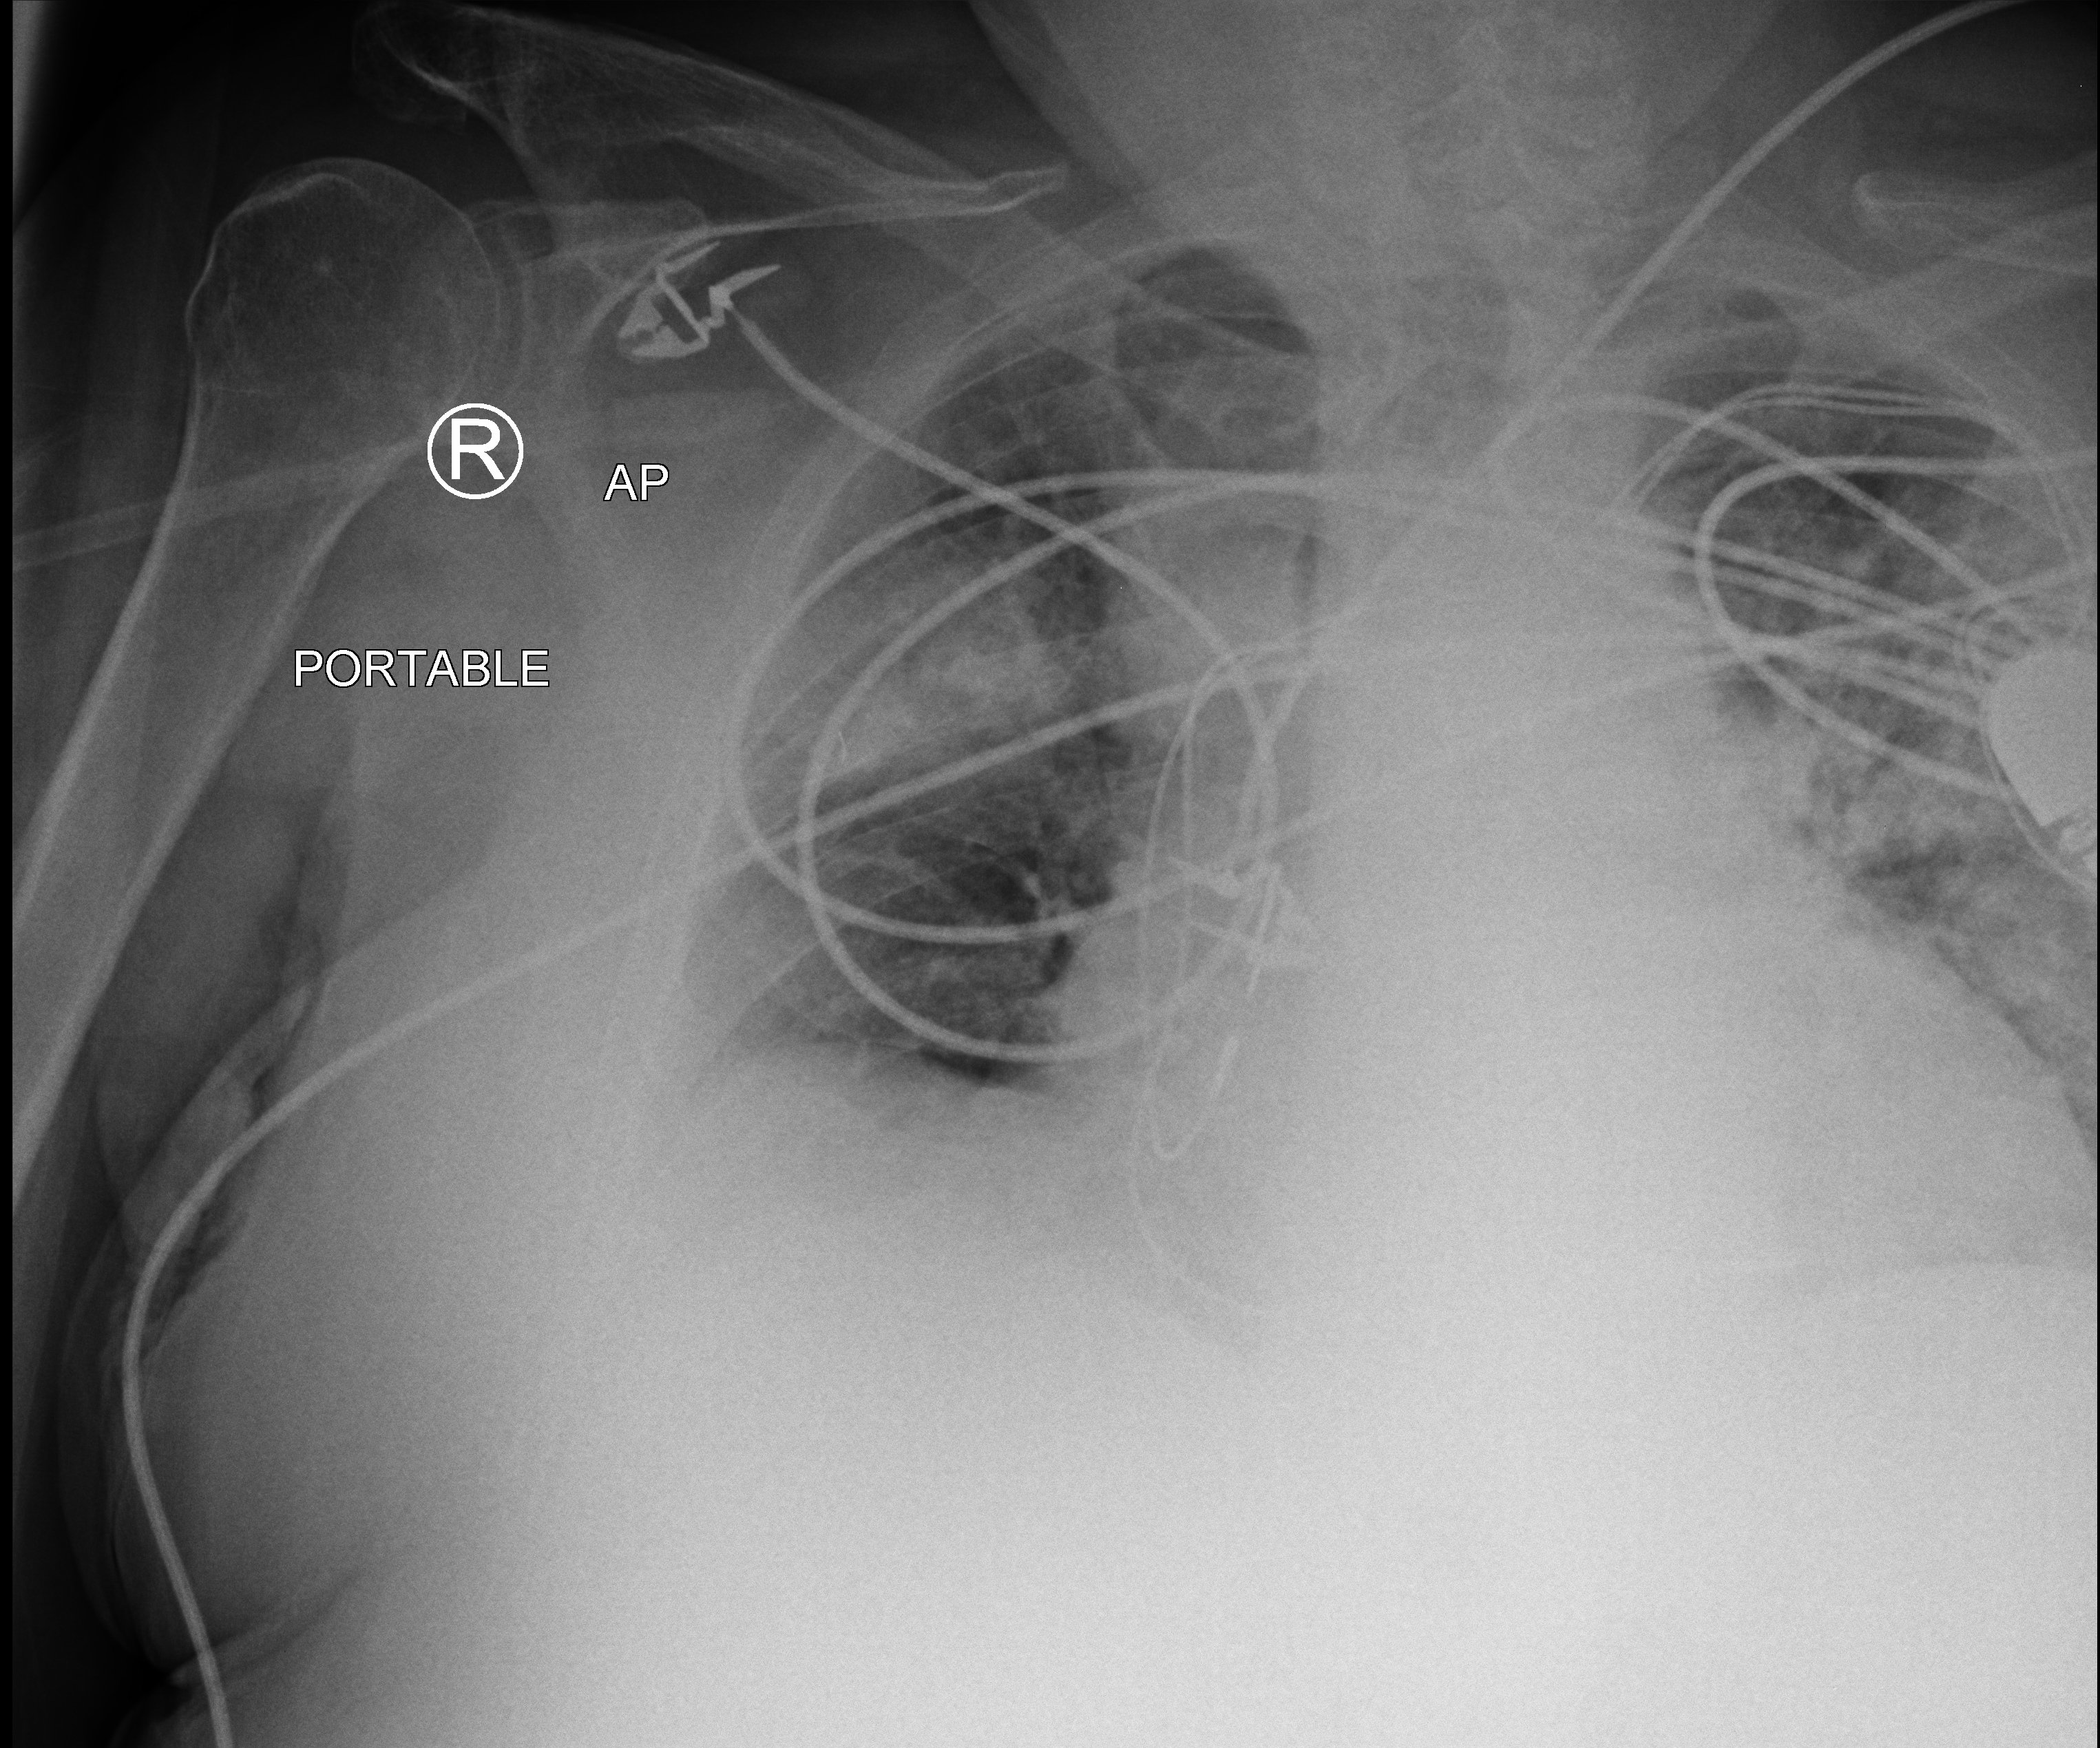
Portable chest radiograph; anteroposterior (AP) projection. Patient hospitalised with COVID-19; male, aged 75–90 years.
Admission-level facts for this patient (not findings on this image; timing relative to this image not recorded): chronic kidney disease (admission record): no; length of hospital stay: 15 days.